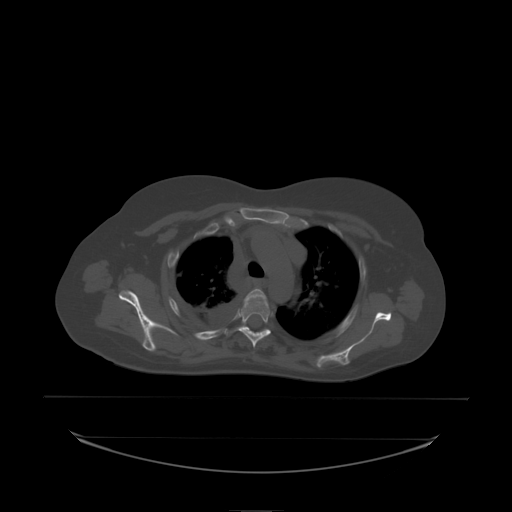
CT including the spine, one axial slice; slice 167 of 242 in the series (ordered by position); bone window (W 1800 / L 400 HU); 2.5 mm slice thickness; 512 × 512 image matrix, field of view 500 × 500 mm. Female patient, age 53 years. Case-level facts recorded for this patient, not image findings: primary cancer: lung.
Outlined on this slice (semi-automatic segmentation, software-assisted and operator-edited):
- T3 vertebra: bounding box [x1, y1, x2, y2] px = [245, 289, 267, 301]
- T4 vertebra: [230, 297, 271, 338]